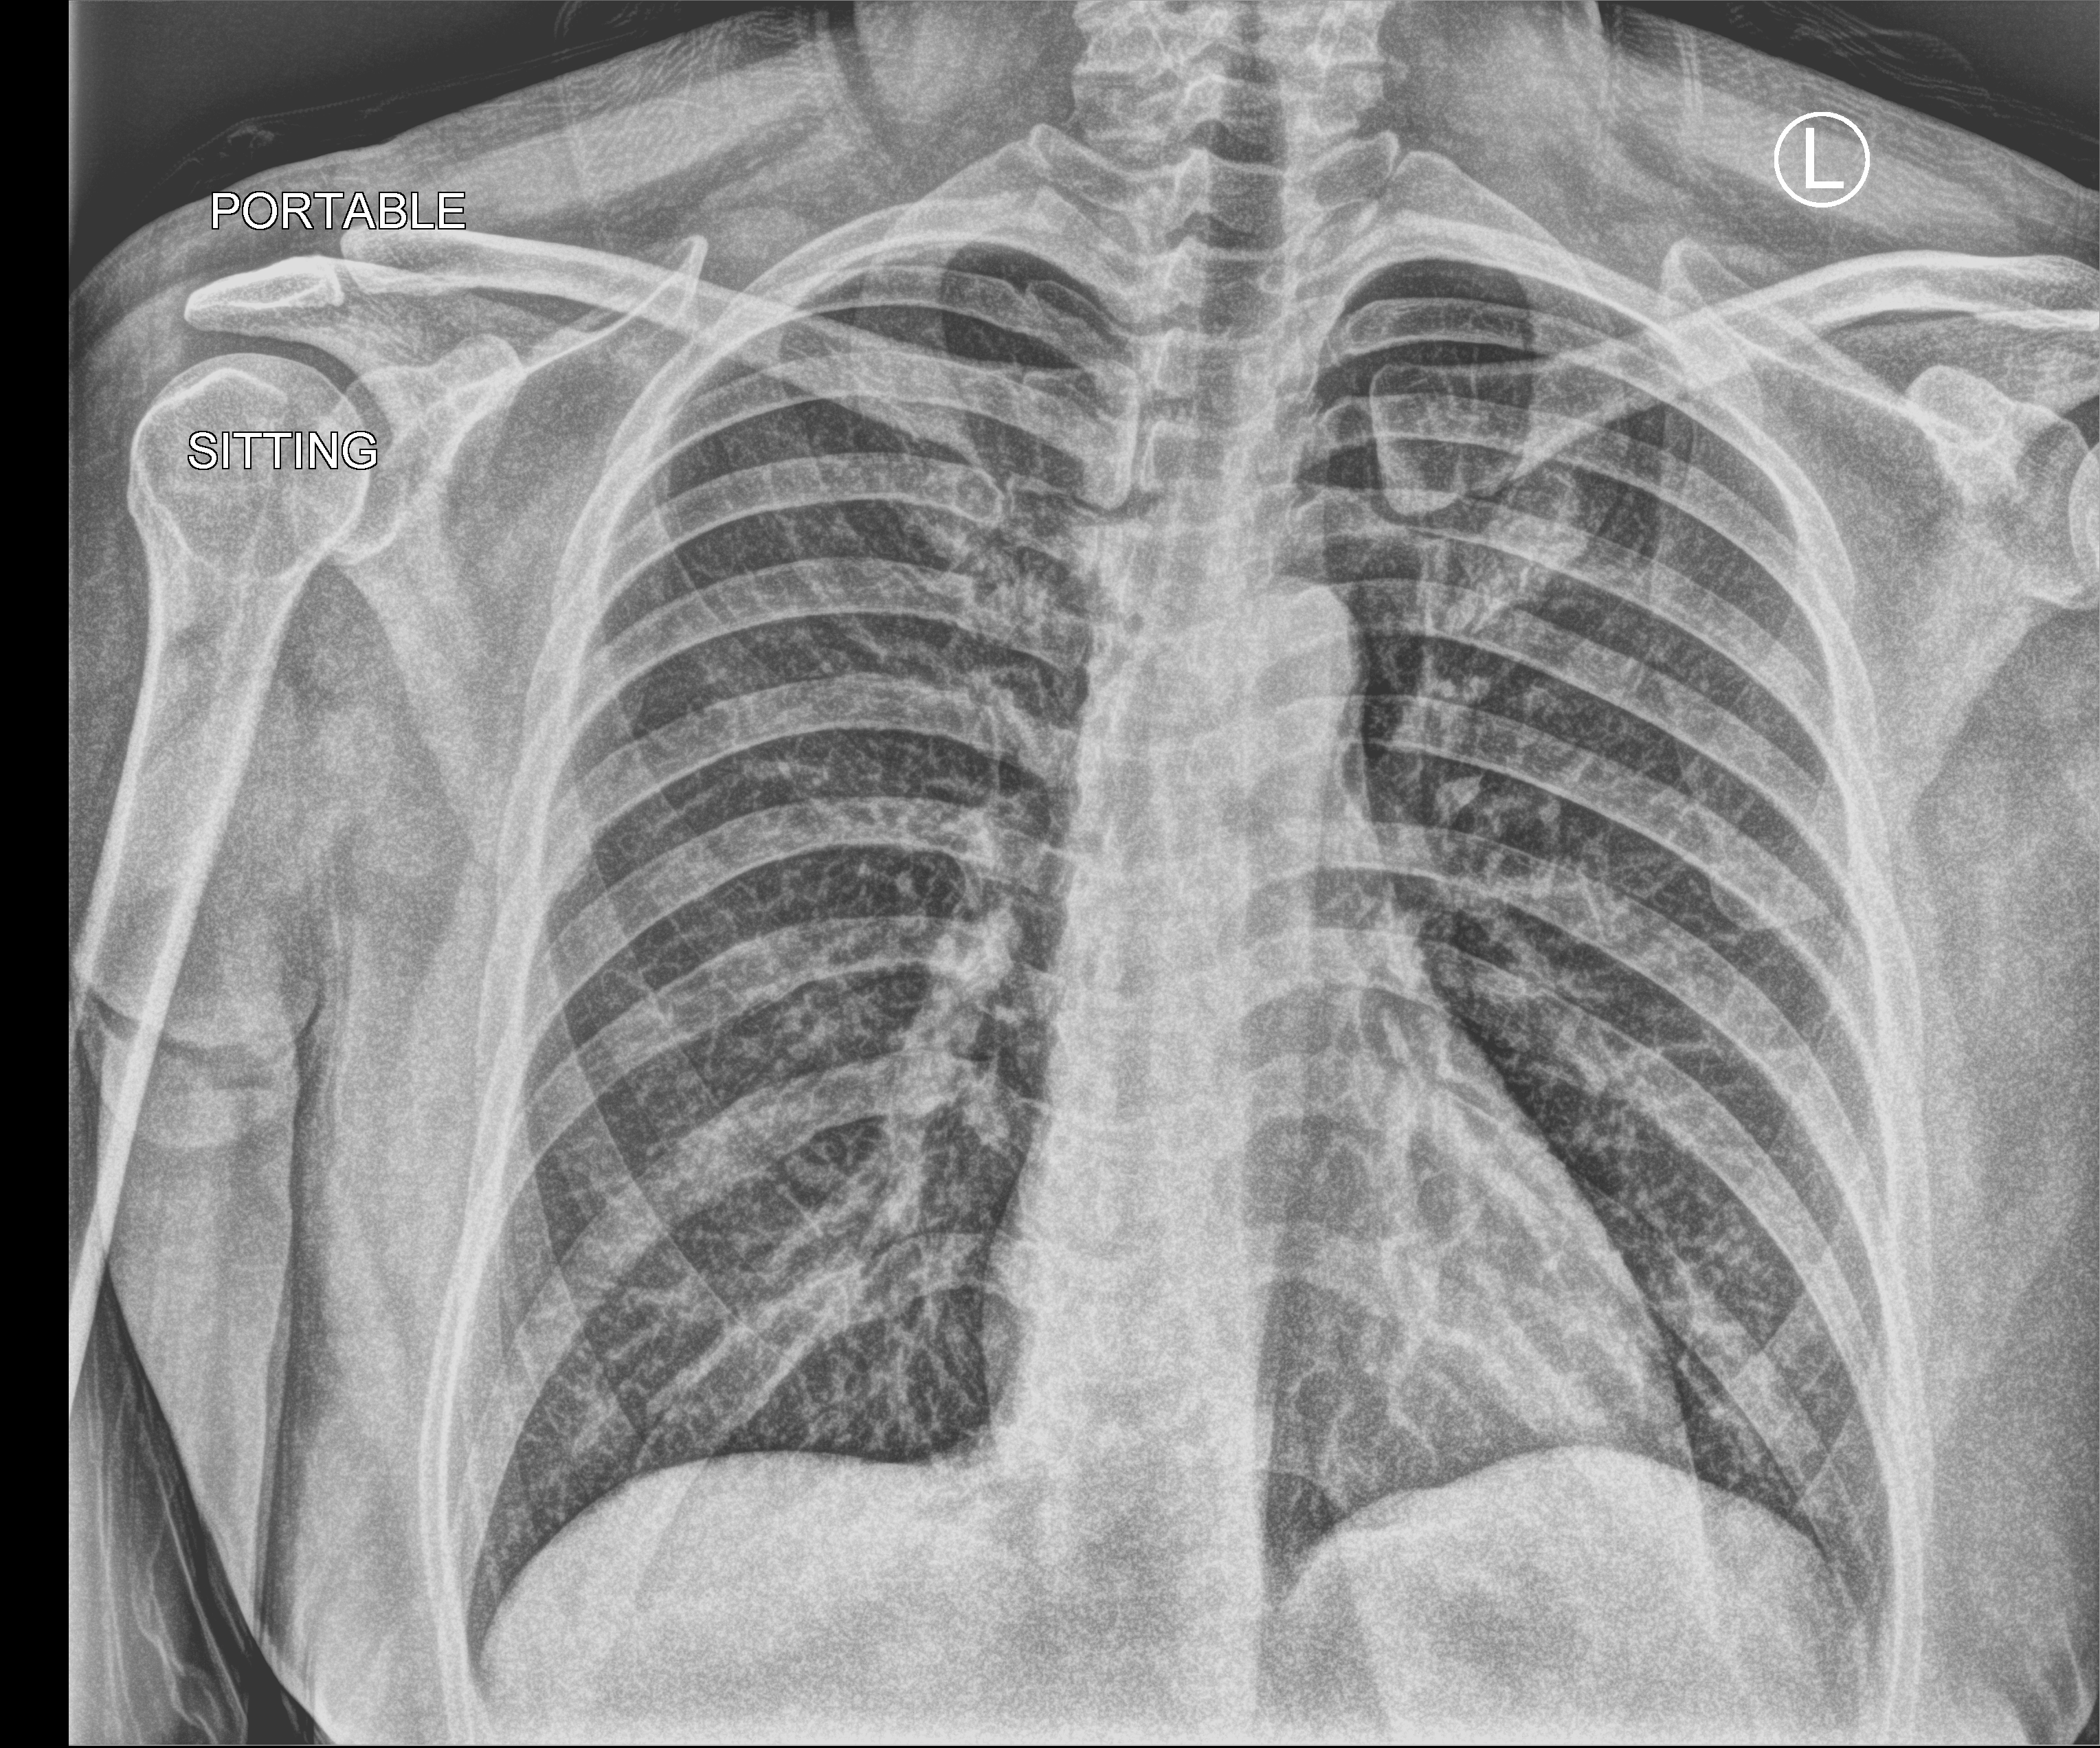
Chest X-ray (portable); anteroposterior (AP) projection. Female patient hospitalised with COVID-19, age 18–59 years.
Admission-level facts for this patient (not findings on this image; timing relative to this image not recorded): admitted to intensive care during this hospital stay: no; smoking status (admission record): never; length of hospital stay: 1 day.